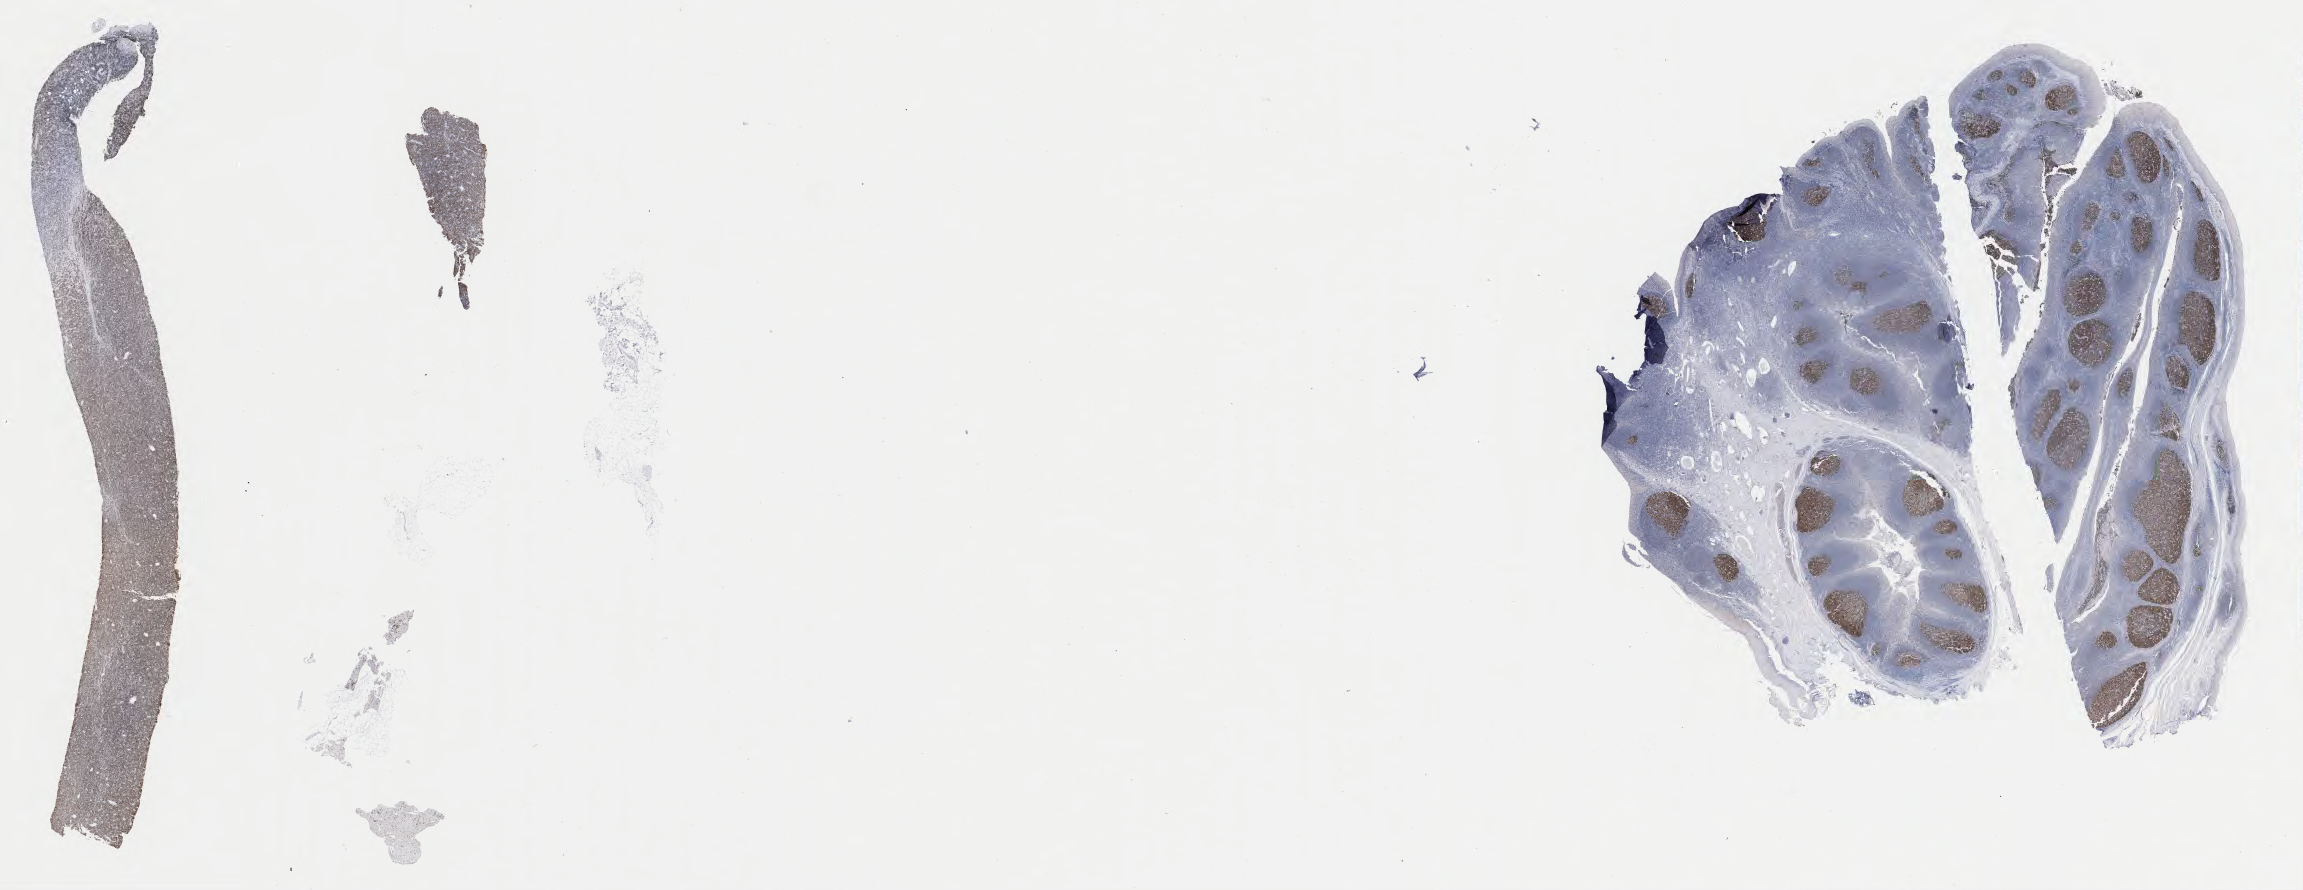
IHC for BCL6, whole-slide image — shown as a low-resolution overview of the whole scanned area (about 37.2 x 14.4 mm), tumor tissue. Patient female; 61 years old.
Histologic diagnosis: Burkitt lymphoma, NOS.